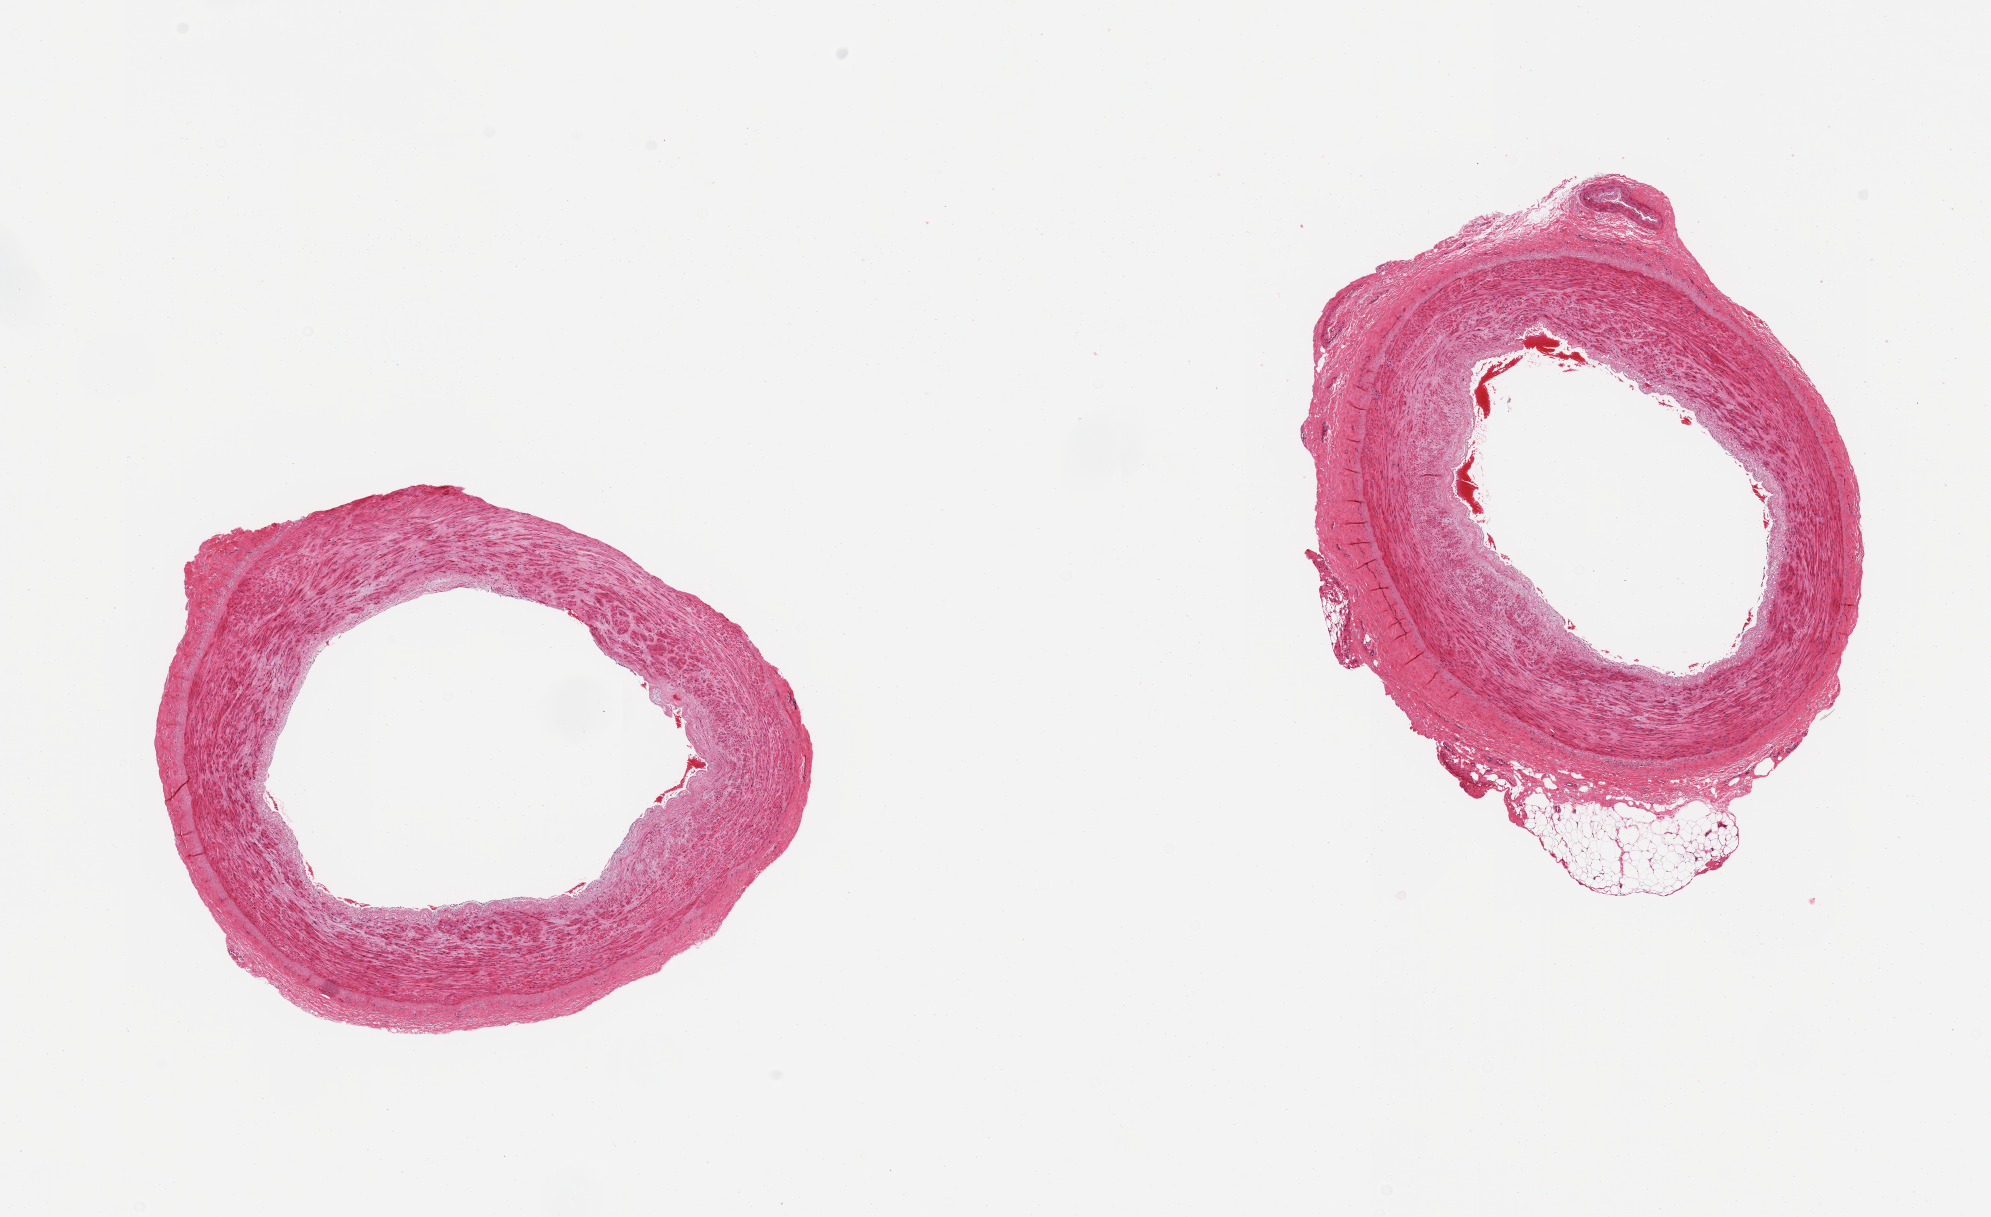
Whole-slide image, hematoxylin and eosin (H&E) stain — whole scanned area (about 15.8 x 9.6 mm) shown as a low-resolution overview; PAXgene-fixed paraffin-embedded (PFPE) section; target tissue: tibial artery; tissue donor sample. Donor: female.
Reviewer comment on this tissue sample: 2 pieces, trace nubbin of adherent fat; trace atherosis.